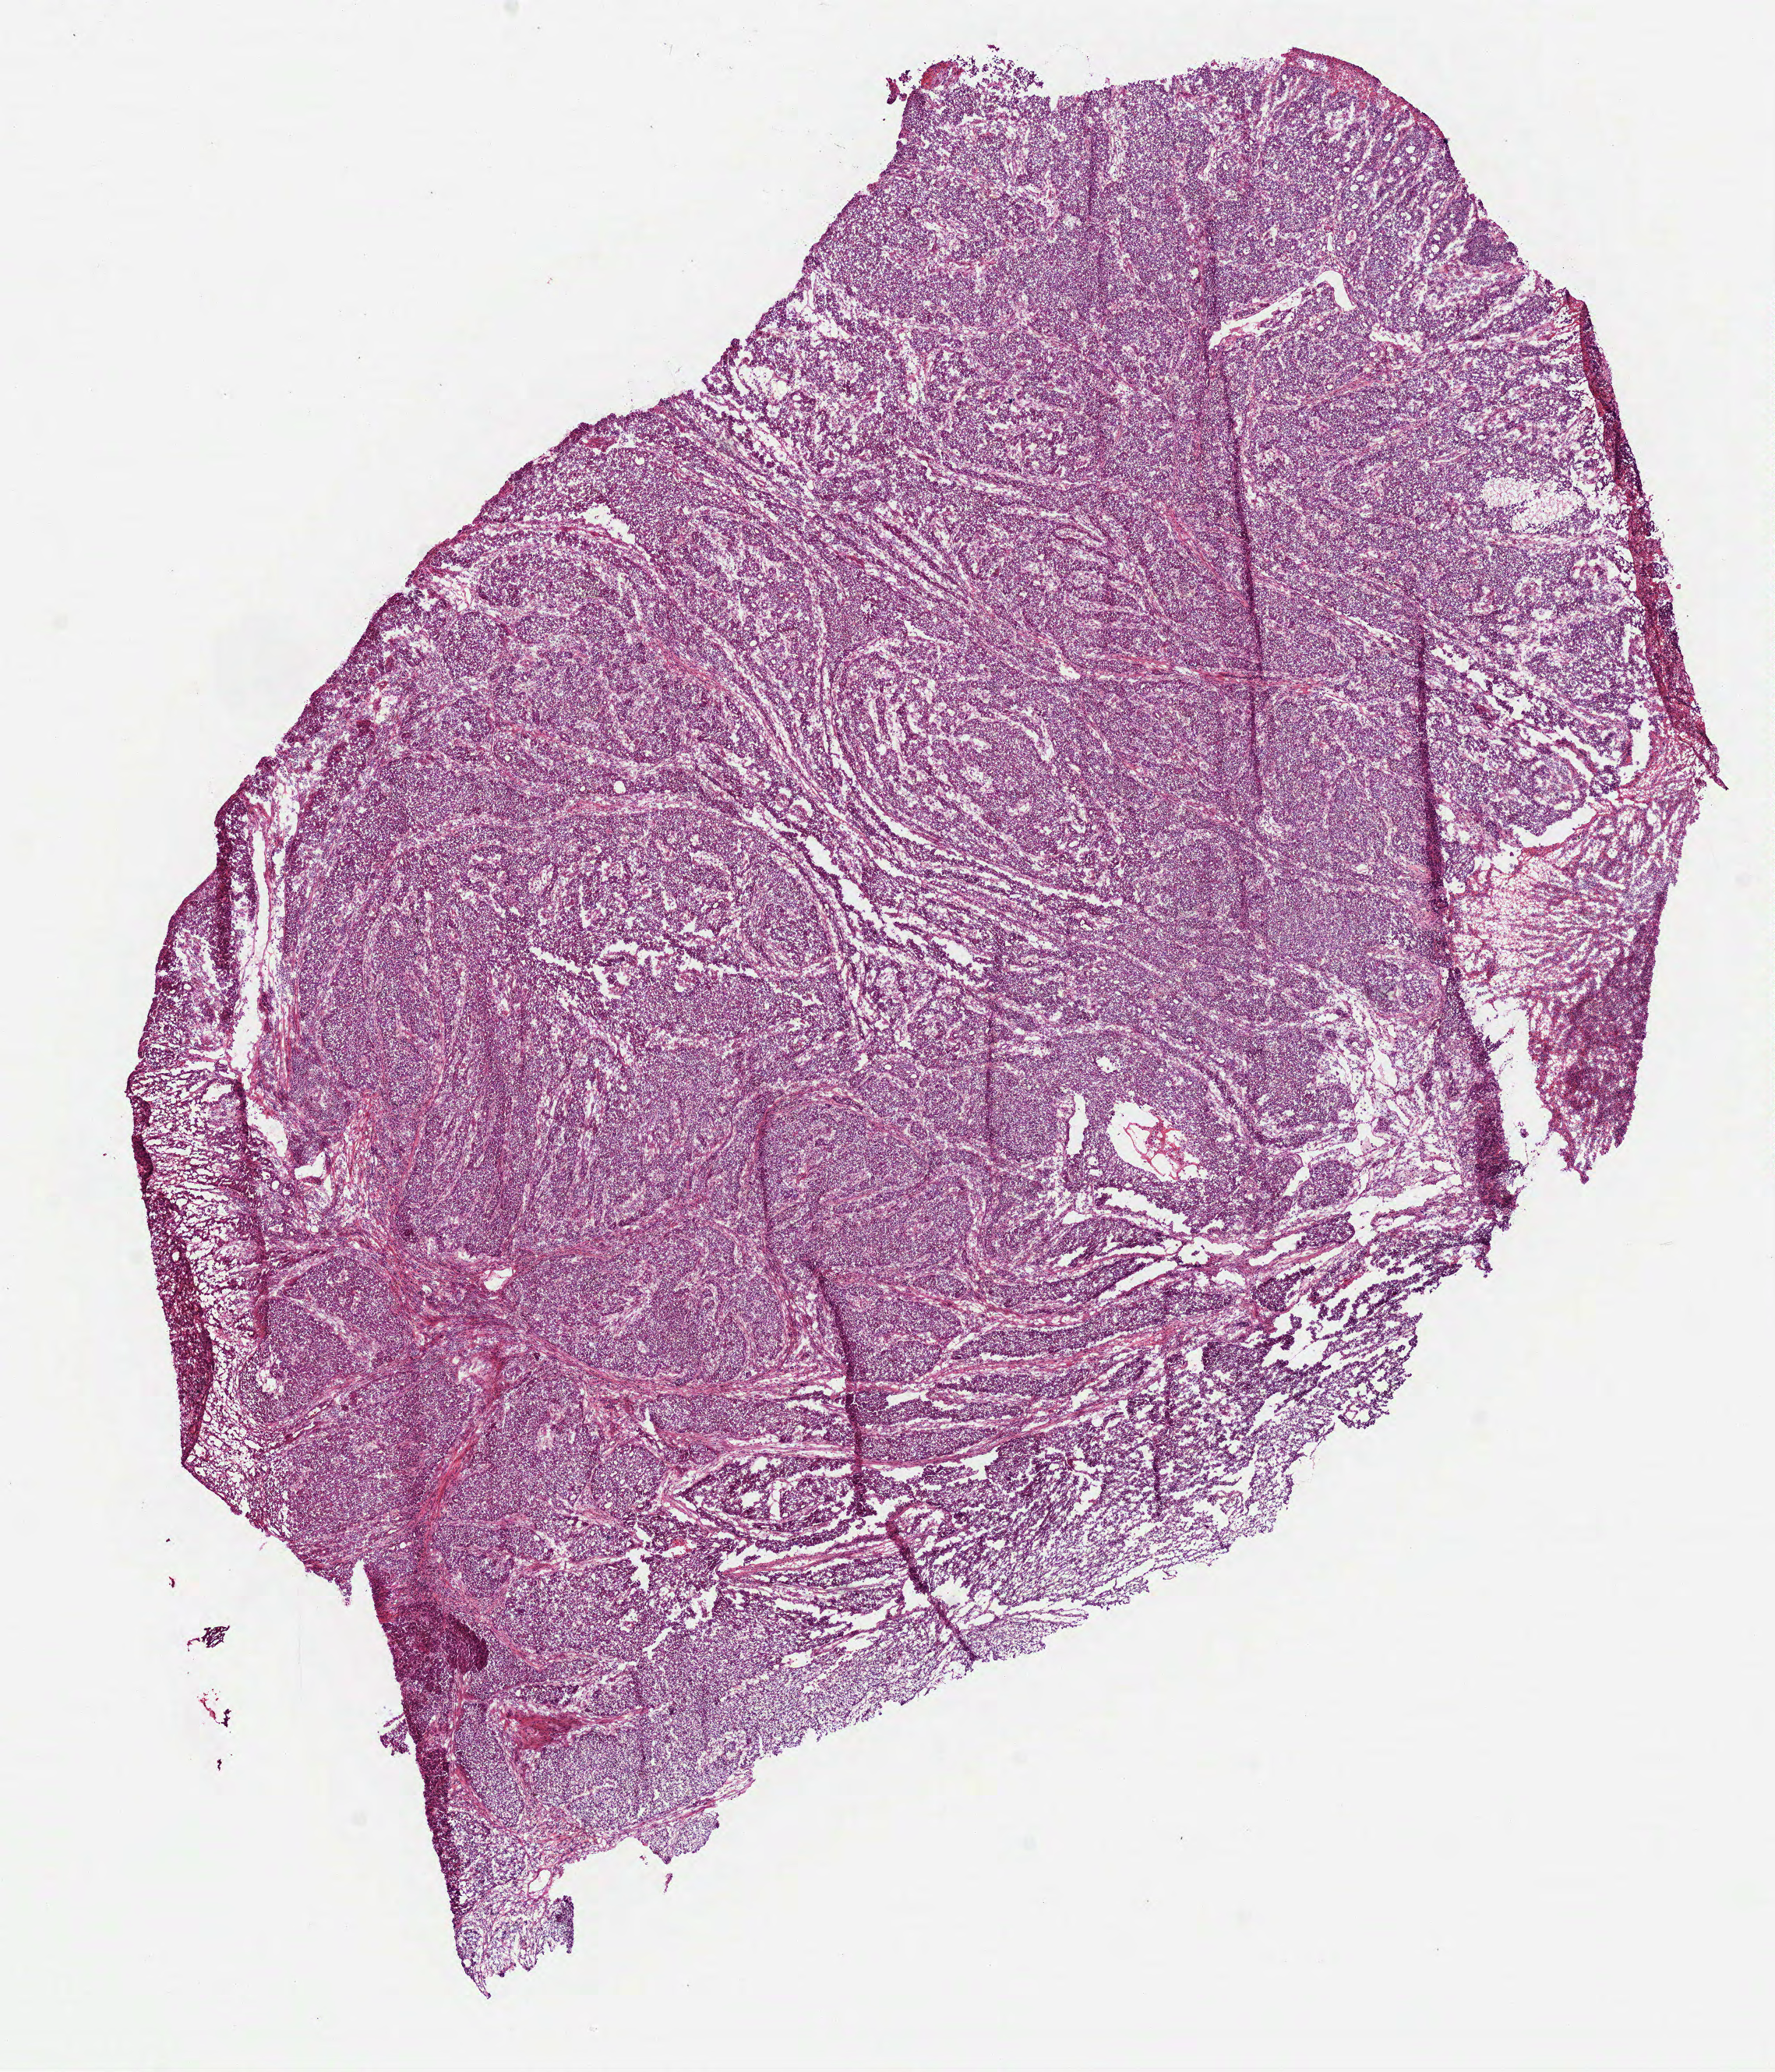
Digitized H&E tissue section (whole slide) — whole scanned area (about 9.2 x 10.7 mm, acquisition: 40x scan) shown as a low-resolution overview, frozen section from the bottom of the tissue portion, sample: primary tumour, stomach. Patient: female, age at initial diagnosis 69 years. Histologic grade: G3 (poorly differentiated). Slide review estimates, as recorded: tumour cells 90%, tumour nuclei 65%, normal cells 0%, stromal cells 5%, necrosis 5%.
- lymph nodes positive (case pathology): 0 of 3 examined
- AJCC pathologic stage: II (7th edition)
- pathologic diagnosis: Adenocarcinoma, intestinal type (body of stomach)